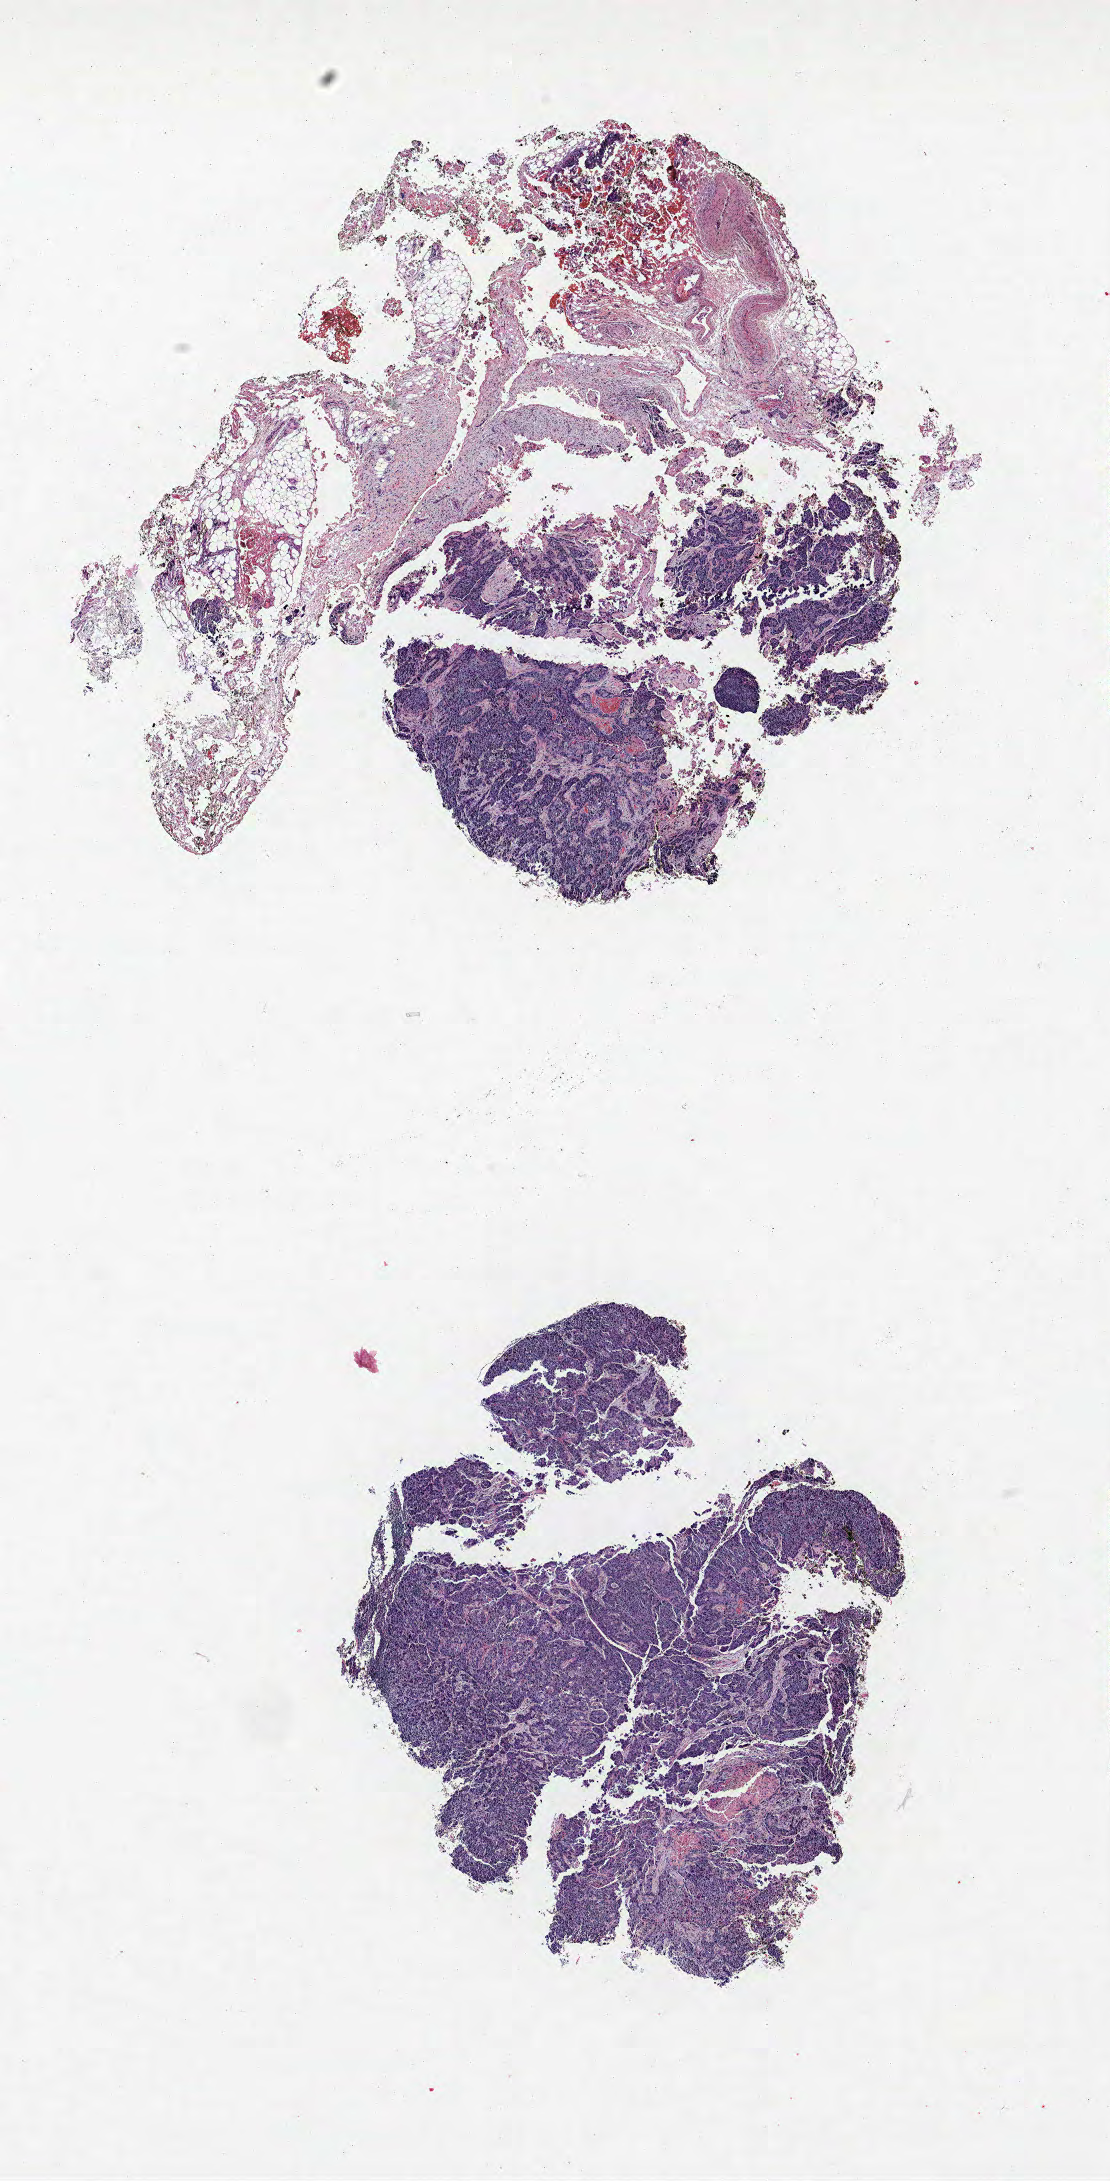
Whole-slide histology image, H&E, low-resolution overview of the scanned area, about 8.9 x 17.5 mm (acquisition: 40x scan); FFPE section; lung tissue. Female patient, aged 63 at enrolment. Former smoker at enrolment. Grade: moderately differentiated (G2).
Tumour size (pathology): 42 mm. Stage (AJCC 6th edition): IIA. Participant's lung-cancer diagnosis: Squamous cell carcinoma, keratinizing, NOS. Primary tumour location (clinical record): right upper lobe.